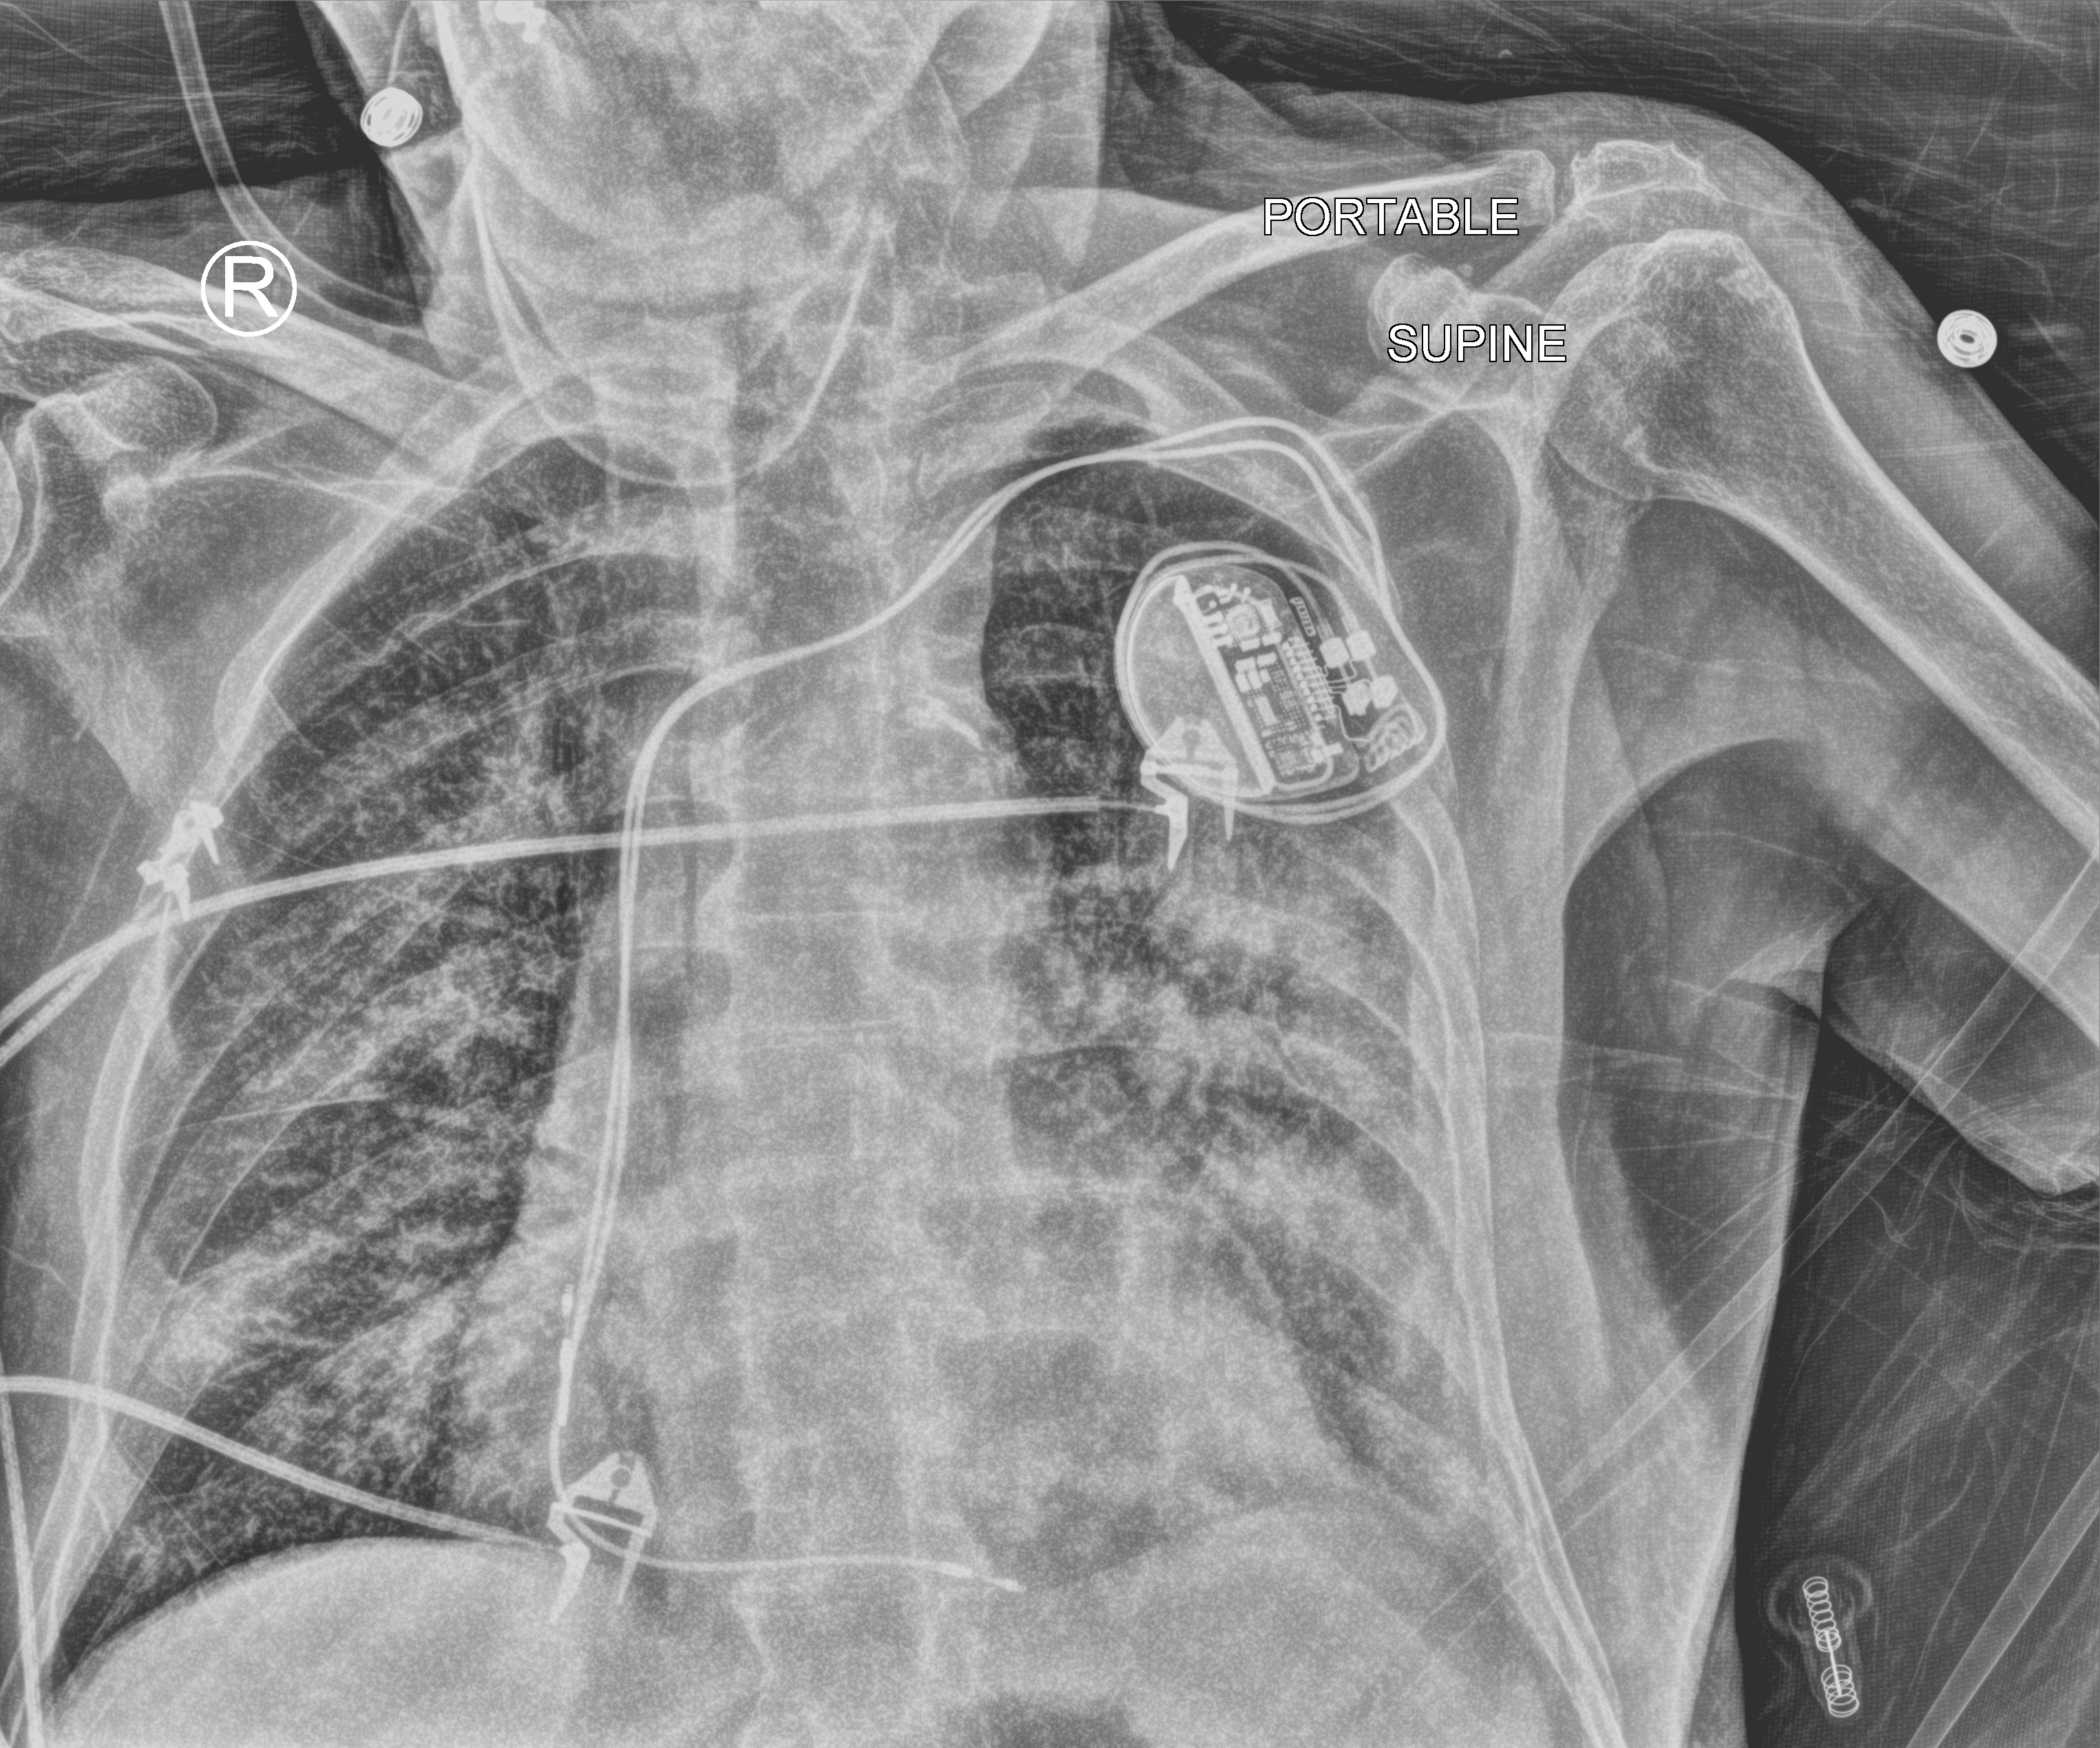
Bedside chest radiograph (computed radiography); anteroposterior (AP) projection. Patient hospitalised with COVID-19; male, aged 75–90 years.
Hospital-stay facts (about this admission, not read from this image; timing relative to this image not recorded):
- admitted to intensive care during this hospital stay: no